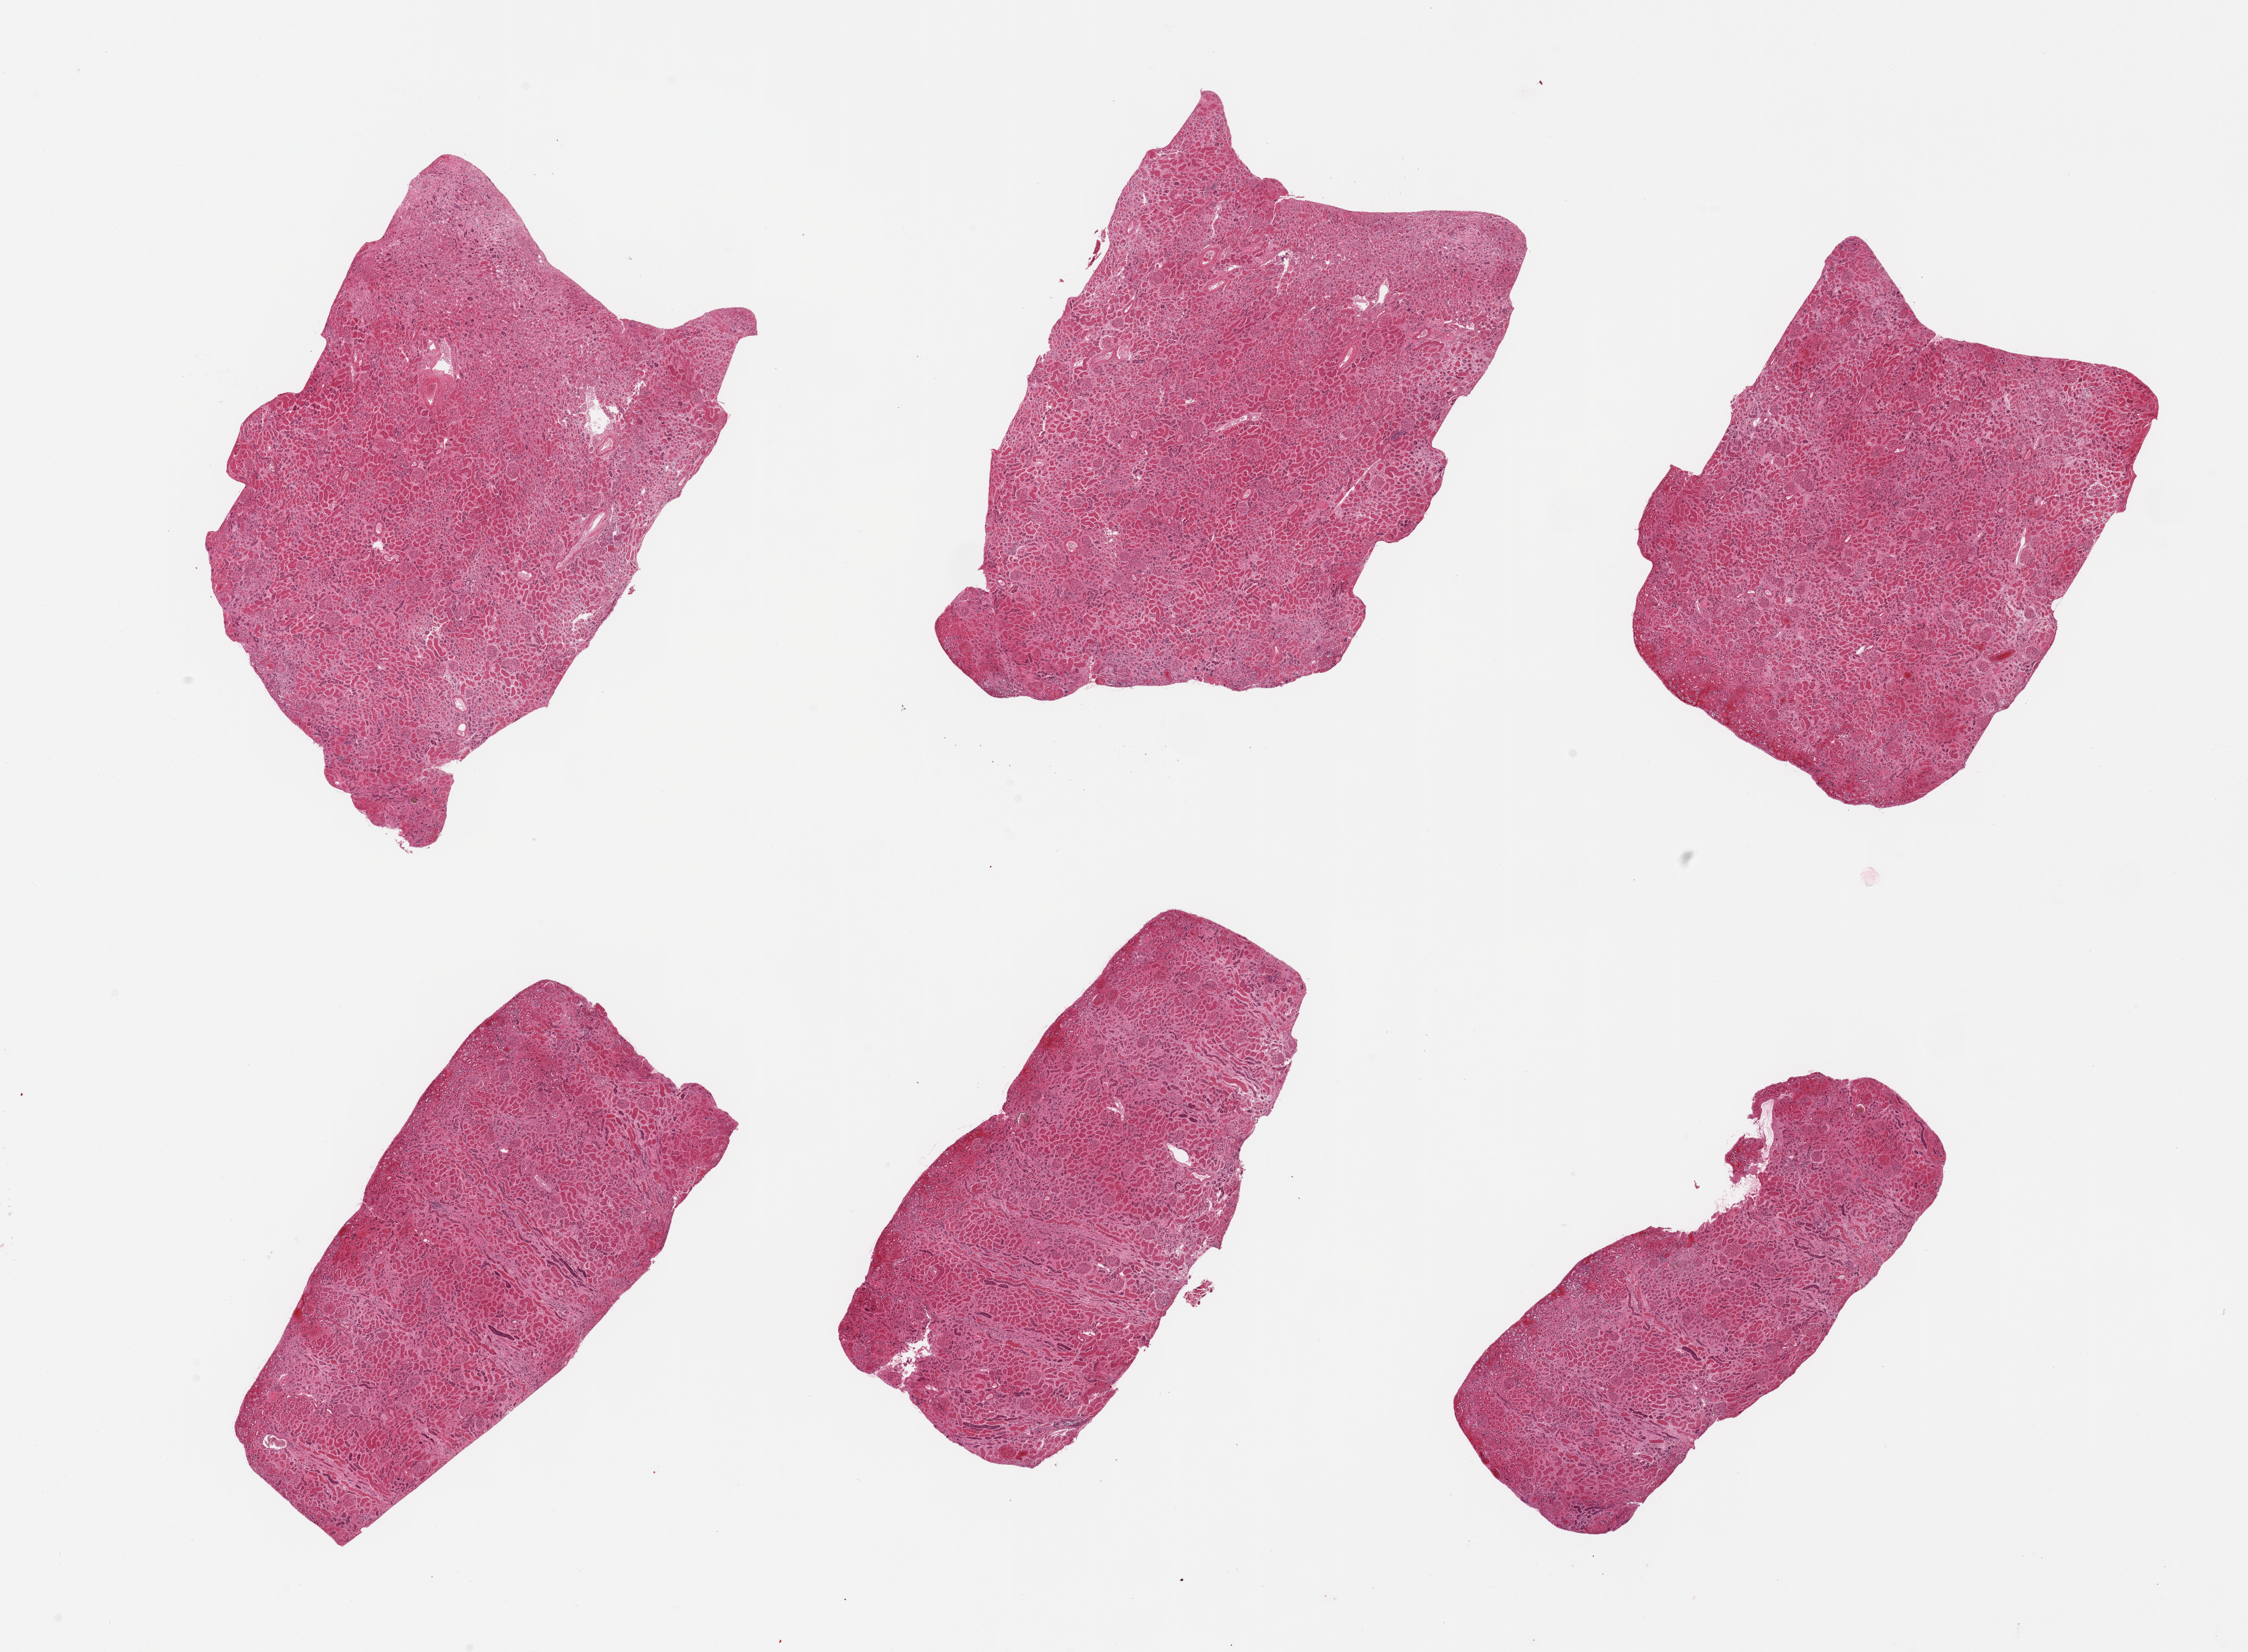
H&E whole-slide image — a low-resolution overview of the entire scanned area, about 26.6 x 19.5 mm (slide scanned at 20x), PAXgene-fixed, paraffin-embedded tissue, section of renal cortex (target tissue), tissue donor sample. Donor: female.
Pathologist's review note for this sample: 6 pieces; predominantly cortex, tubules autolyzed, cannot distinguish from acute tubular necrosis.